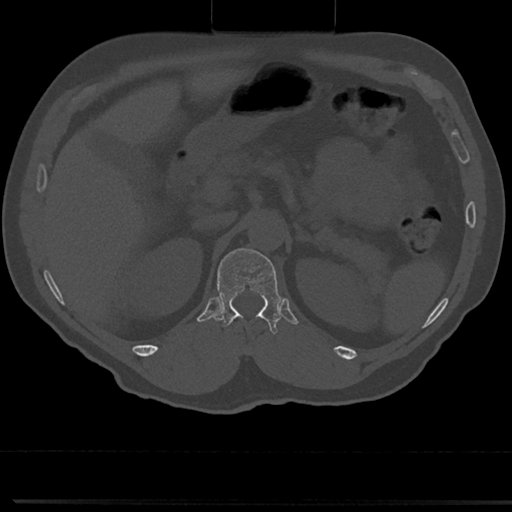
CT including the spine, one axial slice; slice 148 of 817 in the series (ordered by position); reconstruction kernel Br40s/3; bone window (W 1800 / L 400 HU); 512 × 512 image matrix. Male patient, age 61 years. From the clinical record (not read from this slice): primary cancer: prostate.
Outlined on this slice (semi-automatically segmented with operator editing):
- T12 vertebra: bounding box <212,245,279,338> (left, top, right, bottom; pixels)